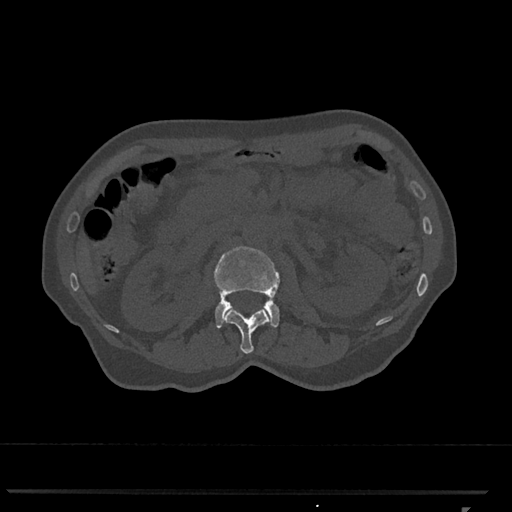
CT including the spine, one axial slice. 120 kVp. Bone window (W 1800 / L 400 HU). 0.5 mm slice thickness. 512 × 512 image matrix, field of view 380 × 380 mm. Patient: female, 62 years. Case-level facts recorded for this patient, not image findings: primary cancer: renal.
Annotated regions visible in this slice (semi-automatically segmented with operator editing):
- L1 vertebra: bounding box <222,306,272,354> (left, top, right, bottom; pixels)
- L2 vertebra: <214,246,280,328>